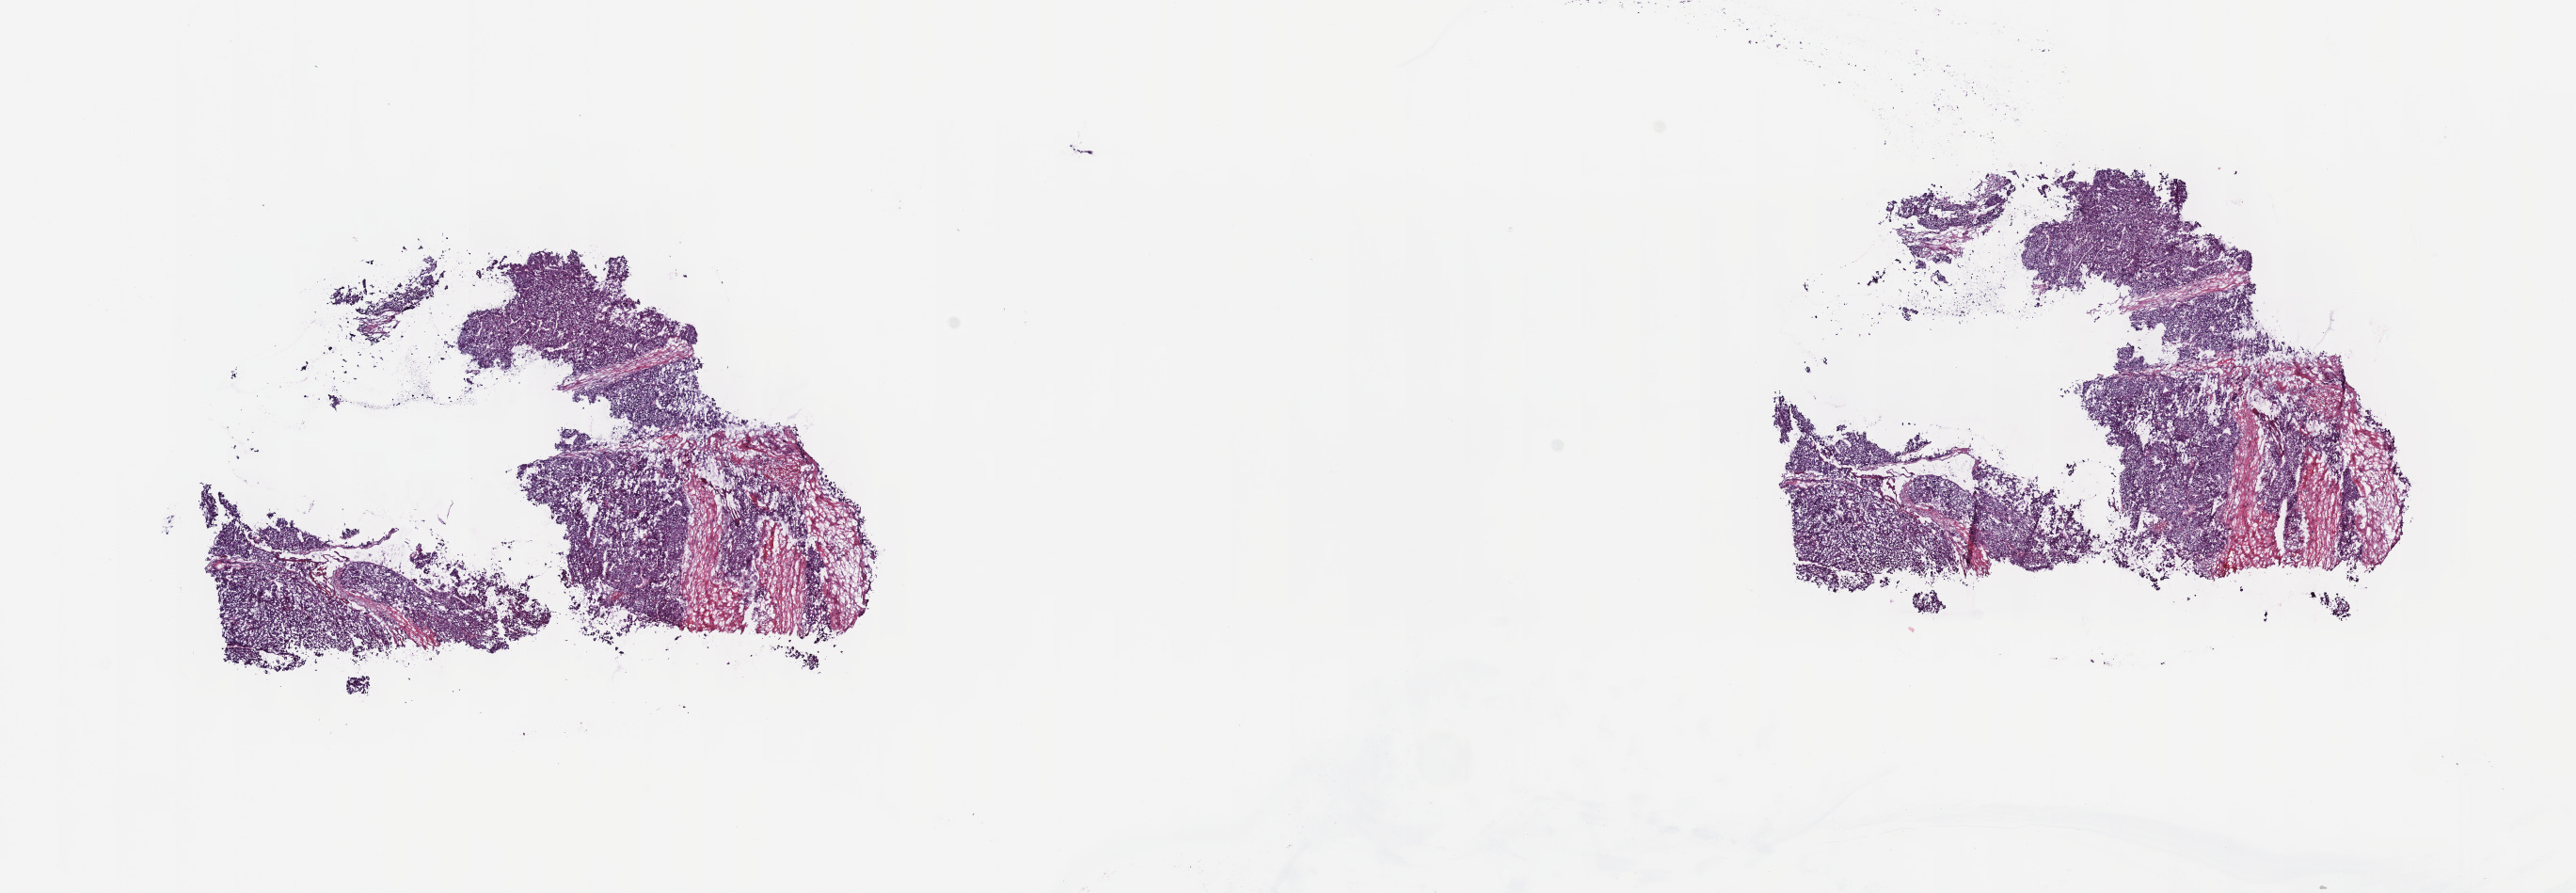
Digitized Hematoxylin and eosin (H&E) stained tissue section (whole slide), a low-resolution overview of the entire scanned area, about 22.1 x 7.7 mm; frozen section from the top of the tissue portion; primary tumour sample from the liver. Female, age 39 years at initial diagnosis. Histologic grade: G3 (poorly differentiated). Pathologist review of this section (percent, as recorded): tumour cells 90%, tumour nuclei 94%, normal cells 0%, stromal cells 10%, necrosis 0%. Infiltration values recorded for this section: lymphocyte infiltration 0%, monocyte infiltration 0%, neutrophil infiltration 0%.
AJCC pathologic stage: IIIA (6th edition). Histologic diagnosis: Hepatocellular carcinoma, NOS. TNM: T3 N0 M0.